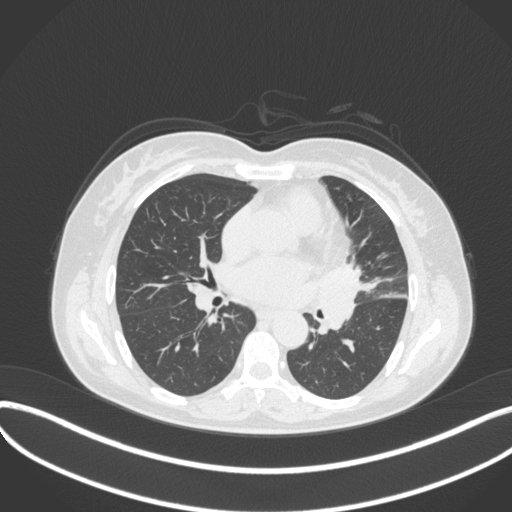
Chest CT, one axial slice. Position 179 of 373 along the scan axis. Lung window (W 1500 / L -600 HU). 1 mm slice thickness. 512 × 512 image matrix, field of view 400 × 400 mm. Patient: female, 54 years. From the clinical record (not read from this slice): clinical TNM (as recorded): T2a N1 M0; histopathological grade: G3.
Structures marked on this image (rectangle marked by the reading radiologist):
- lung tumour (recorded histology: small cell carcinoma): box from (x=317, y=253) to (x=371, y=339) px